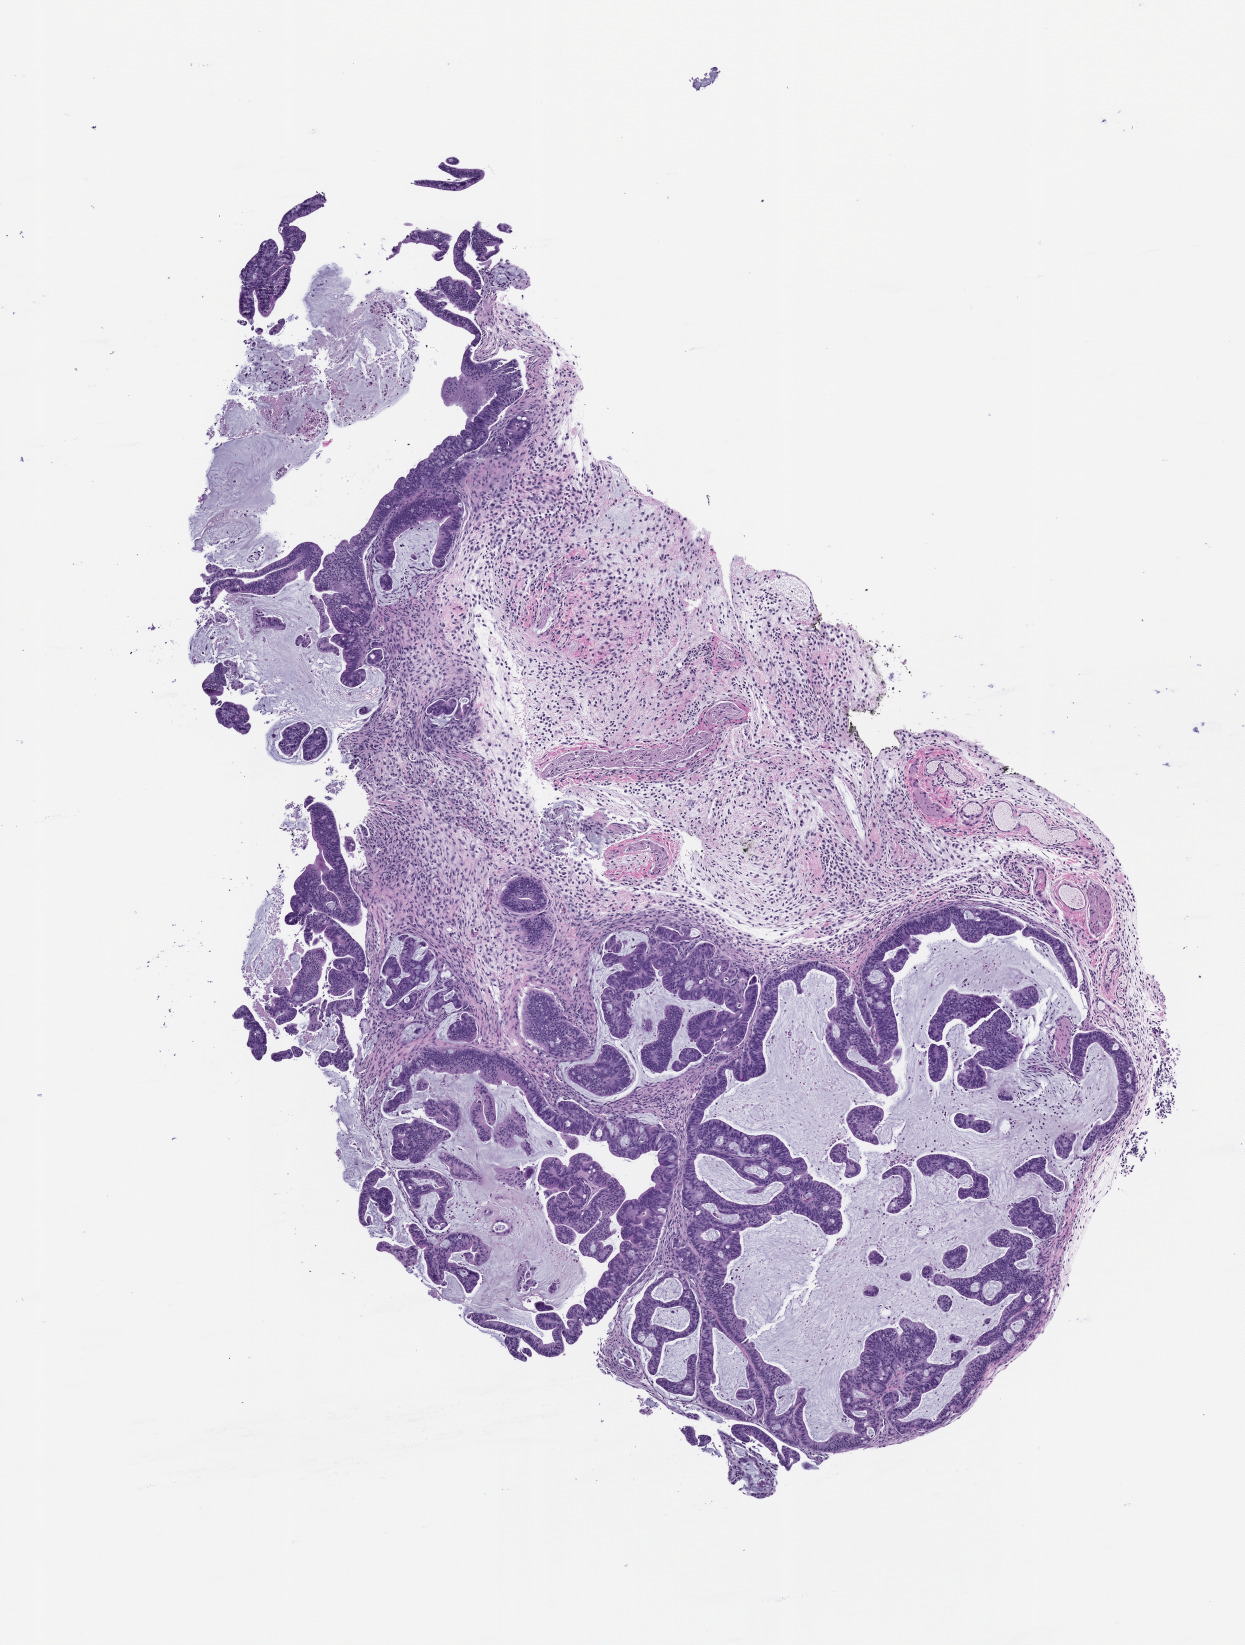
Whole-slide image, H&E: patient-derived xenograft (human tumor grown in a mouse), passage 1 — low-resolution overview of the scanned area, about 5.0 x 6.6 mm. Formalin-fixed paraffin-embedded section. Tumor site category: rectum.
• originating patient diagnosis: Rectal Adenocarcinoma